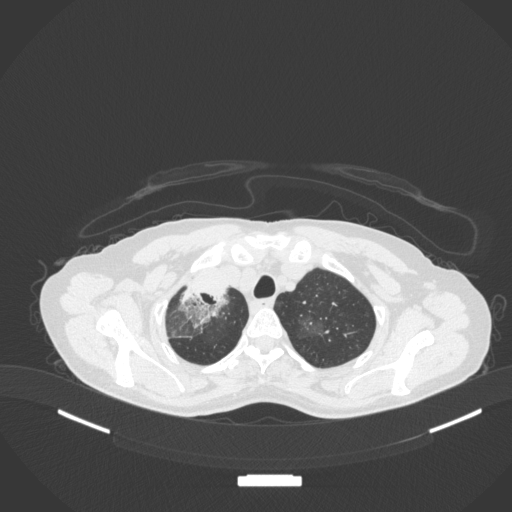
Chest CT, one axial slice. Position 278 of 311 along the scan axis. 120 kVp. Lung window (W 1500 / L -600 HU). 512 × 512 image matrix. Patient: female, 59 years. Case-level facts recorded for this patient, not image findings: clinical TNM (as recorded): T3 N0 M0; histopathological grade: G1.
Structures marked on this image (bounding box drawn by a radiologist):
- lung tumour (recorded histology: adenocarcinoma): bounding box [x1, y1, x2, y2] px = [181, 279, 230, 330]